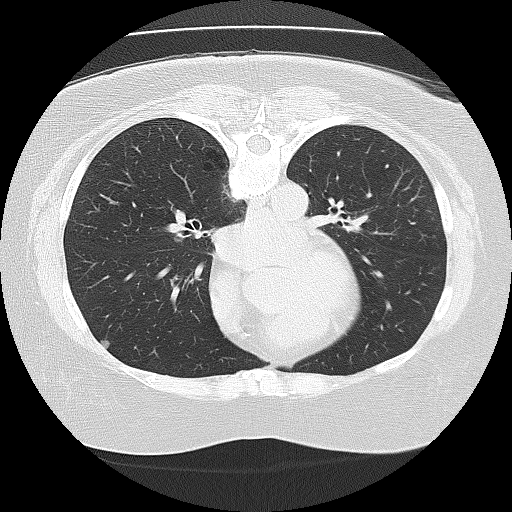
Axial slice from a low-dose chest CT screening exam, second screening round (one year after baseline), lung window (W 1500 / L -600 HU), reconstruction kernel FC30 (as recorded), 512 × 512 image matrix. Female participant, aged 67 years at enrolment. Former smoker at enrolment.
• Lesion marked by an expert reader, bounding box <87,329,128,361> (left, top, right, bottom; pixels).
• Screening reader's record for this exam (one nodule recorded; not confirmed to be the boxed lesion): non-calcified nodule or mass ≥4 mm, right middle lobe, 5 × 5 mm, smooth margins, soft tissue attenuation, pre-existing on the prior screen: yes; interval growth: no.
• Official screen result: positive, no significant change: stable abnormalities potentially related to lung cancer, unchanged since the prior screening exam.
• Lung cancer was diagnosed 247 days after this screen: small cell carcinoma, NOS, right upper lobe, undifferentiated (G4), stage IV (AJCC 6th edition), 60 mm at pathology.